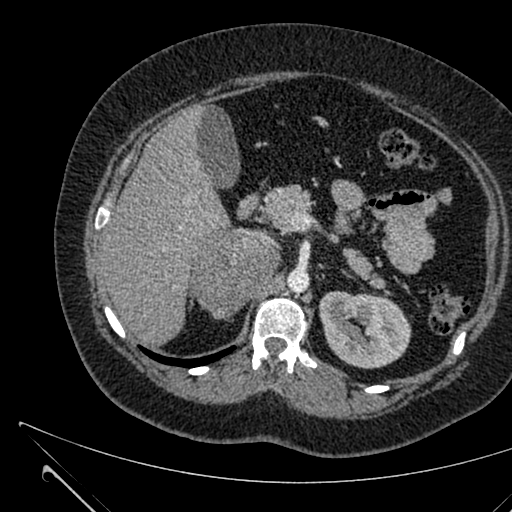
Contrast-enhanced abdominal CT, one axial slice. Slice 410 of 731 in the series (ordered by position). Intravenous contrast given. Soft-tissue window (W 400 / L 40 HU). 512 × 512 image matrix. Female patient, age 36 years. Case-level facts recorded for this patient, not image findings: diagnosis: adrenocortical carcinoma; tumour side: right adrenal; tumour size at pathology: 10 cm; Ki-67 index: 20 %; stage (as recorded): 4.
Structures marked on this image (semi-automatic segmentation, software-assisted and operator-edited):
- mass: bounding box (x1, y1, x2, y2) in pixels: (192, 230, 279, 316)